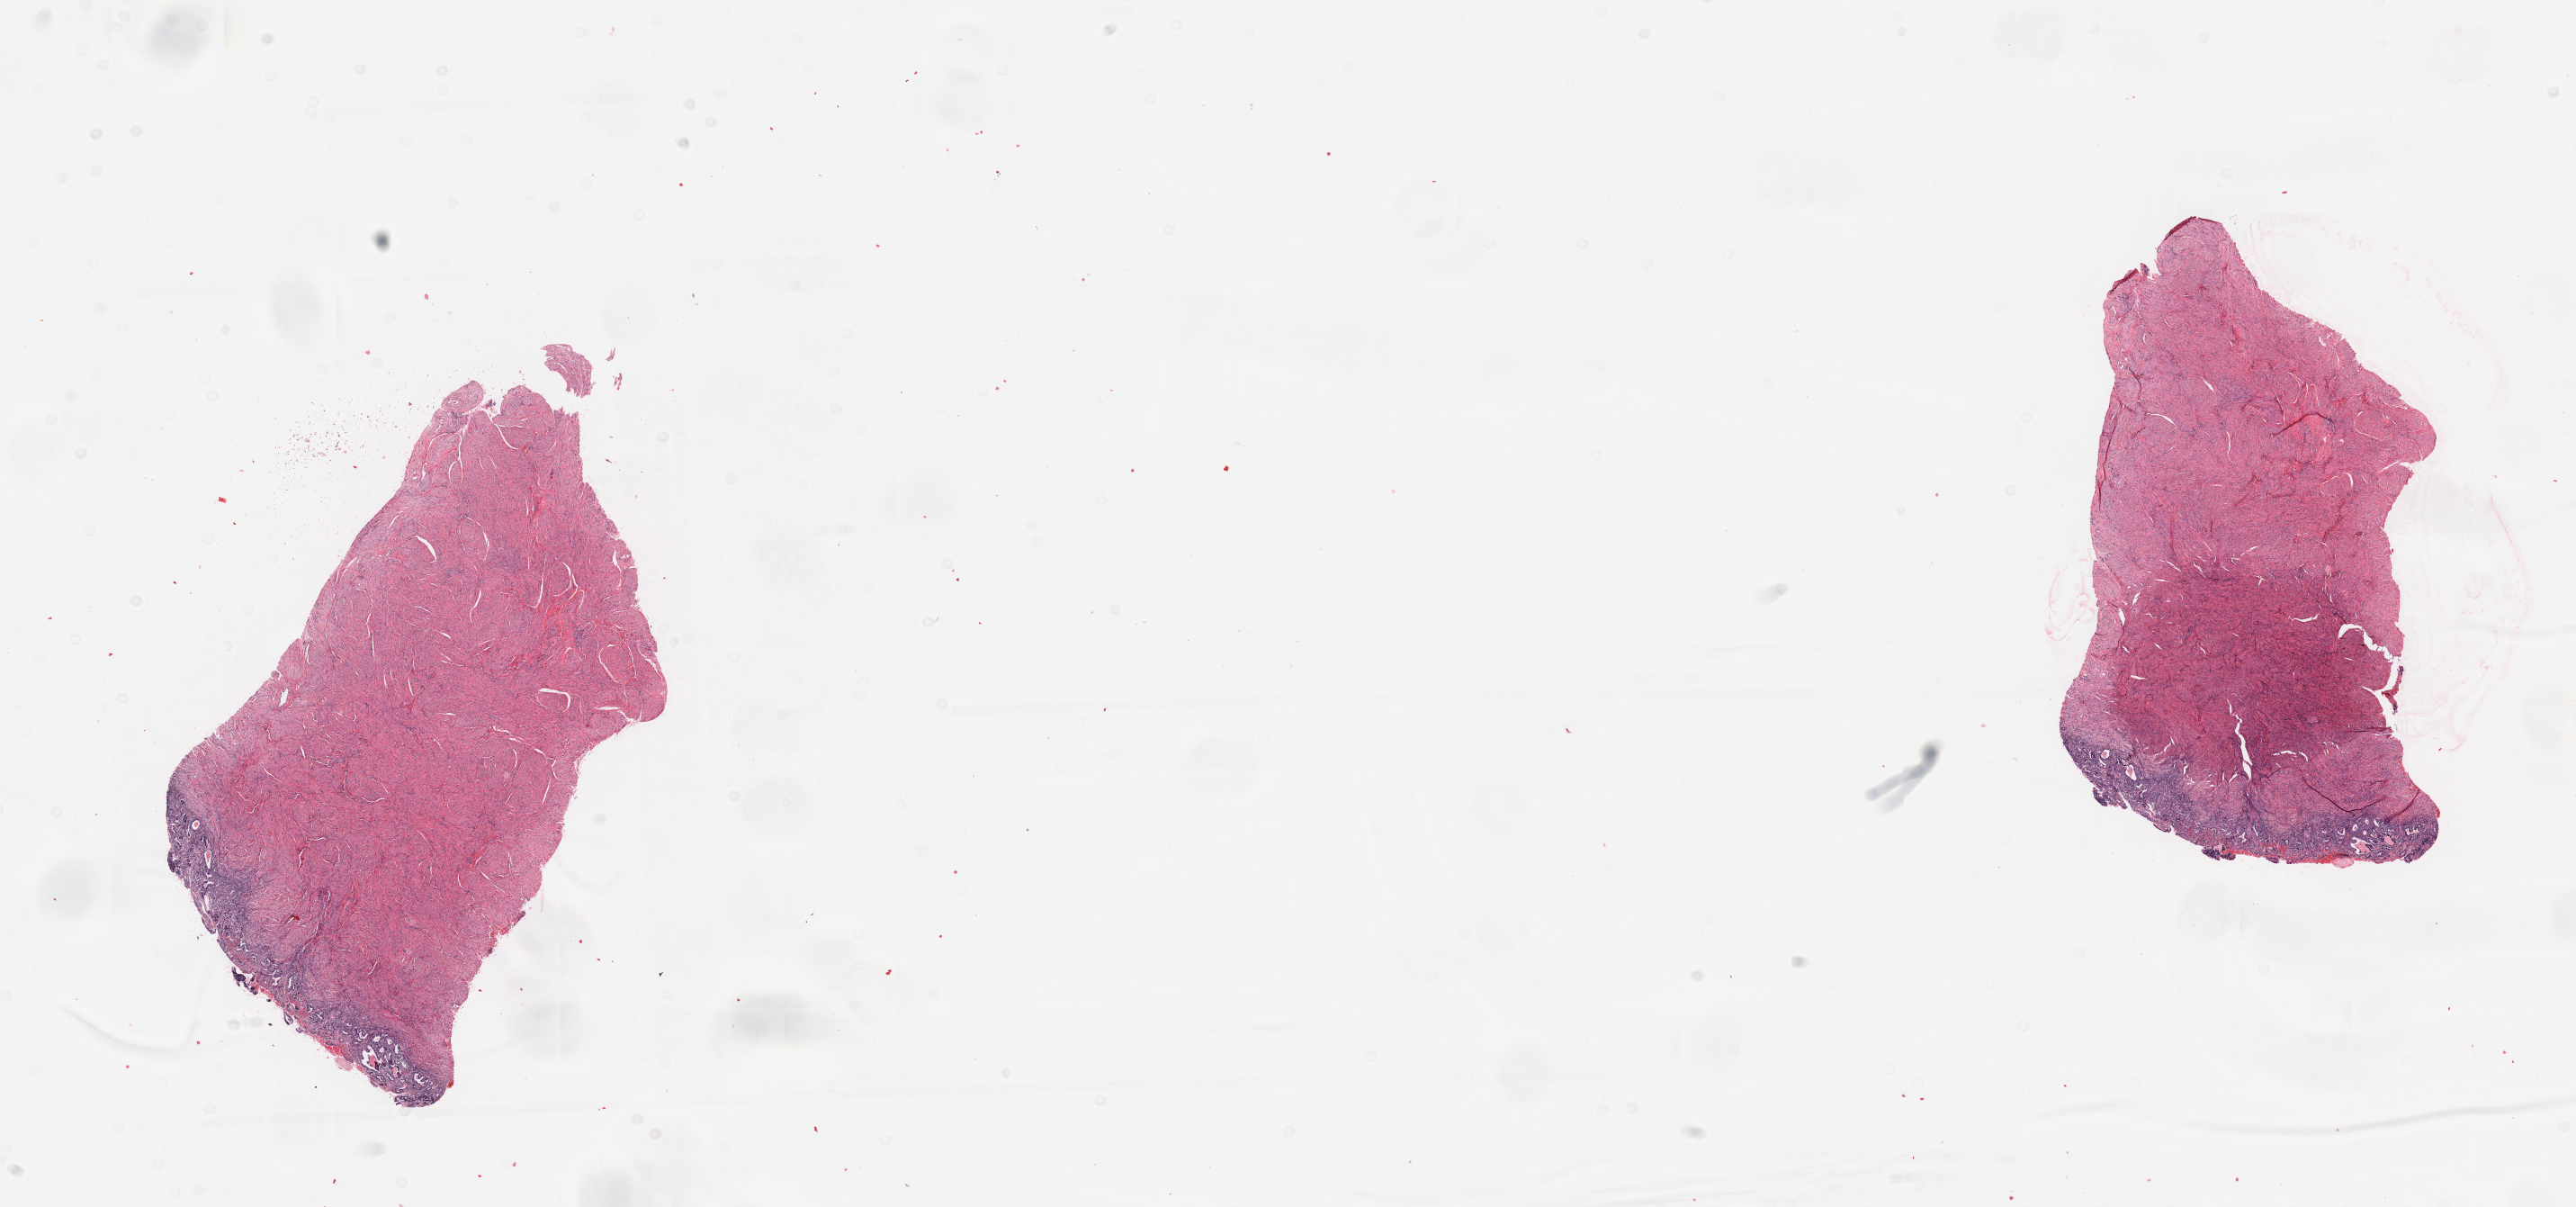
Hematoxylin and eosin (H&E) stained whole-slide image, low-resolution overview of the scanned area, about 22.6 x 10.6 mm (slide scanned at 20x); normal (non-tumour) tissue sample, sampled site: uterus. 51-year-old female patient.
This section: normal (non-tumour) tissue from the same patient. Patient diagnosis: Endometrioid adenocarcinoma, NOS.